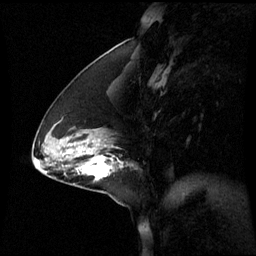
Breast MRI (dynamic contrast-enhanced), one sagittal slice. Slice 24 of 60 in the series (ordered by position). Dynamic contrast-enhanced series, image 2 of 3 at this slice position (ordered by acquisition). 1.5 T. TE 4.2 ms, TR 8.9 ms. 2.2 mm slice thickness. 256 × 256 image matrix. Female patient, age 44 years. Case-level facts recorded for this patient, not image findings: setting: breast cancer imaged before/during neoadjuvant chemotherapy; receptor status: triple-negative.
Structures marked on this image (semi-automatically segmented with operator editing):
- analysis volume of interest (the breast-tissue region the enhancement analysis was run in; not a lesion): bounding box [x1, y1, x2, y2] px = [76, 150, 123, 181]
- tumour enhancement mask (voxels above the 70 % enhancement threshold inside the analysis volume of interest): [83, 156, 112, 181]